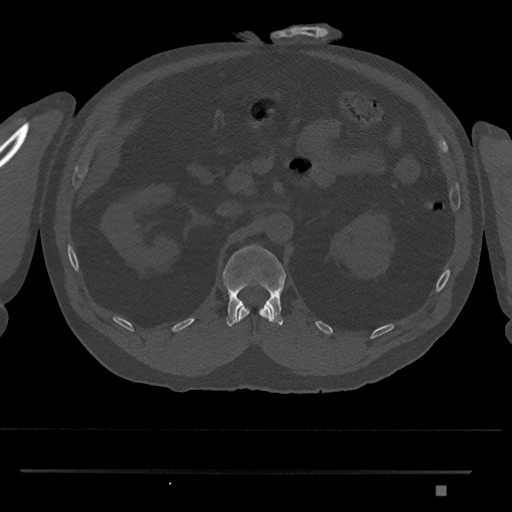
CT including the spine, one axial slice. Position 846 of 1134 along the scan axis. 120 kVp. Bone window (W 1800 / L 400 HU). 512 × 512 image matrix, field of view 429 × 429 mm. Patient: male, 65 years. Case-level facts recorded for this patient, not image findings: primary cancer: prostate.
Outlined on this slice (semi-automatically segmented with operator editing):
- L1 vertebra: box from (x=222, y=244) to (x=286, y=328) px
- T12 vertebra: (x=237, y=305)–(x=272, y=323)